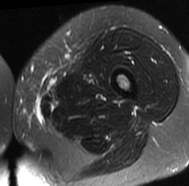
MRI of an extremity soft-tissue mass, one axial slice. Position 15 of 77 along the scan axis. T2-weighted fat-saturated. MR volume resampled by the dataset authors to the PET/CT grid (not the native acquisition matrix). 3.27 mm slice thickness. 189 × 186 image matrix, field of view 185 × 182 mm. Female patient. Case-level facts recorded for this patient, not image findings: histological type: leiomyosarcoma; grade: high; site of the primary tumour: groin.
Annotated regions visible in this slice (expert contour drawn on MRI and transferred to this co-registered scan by the dataset authors):
- gross tumour volume including surrounding oedema: bounding box (x1, y1, x2, y2) in pixels: (15, 106, 43, 123)